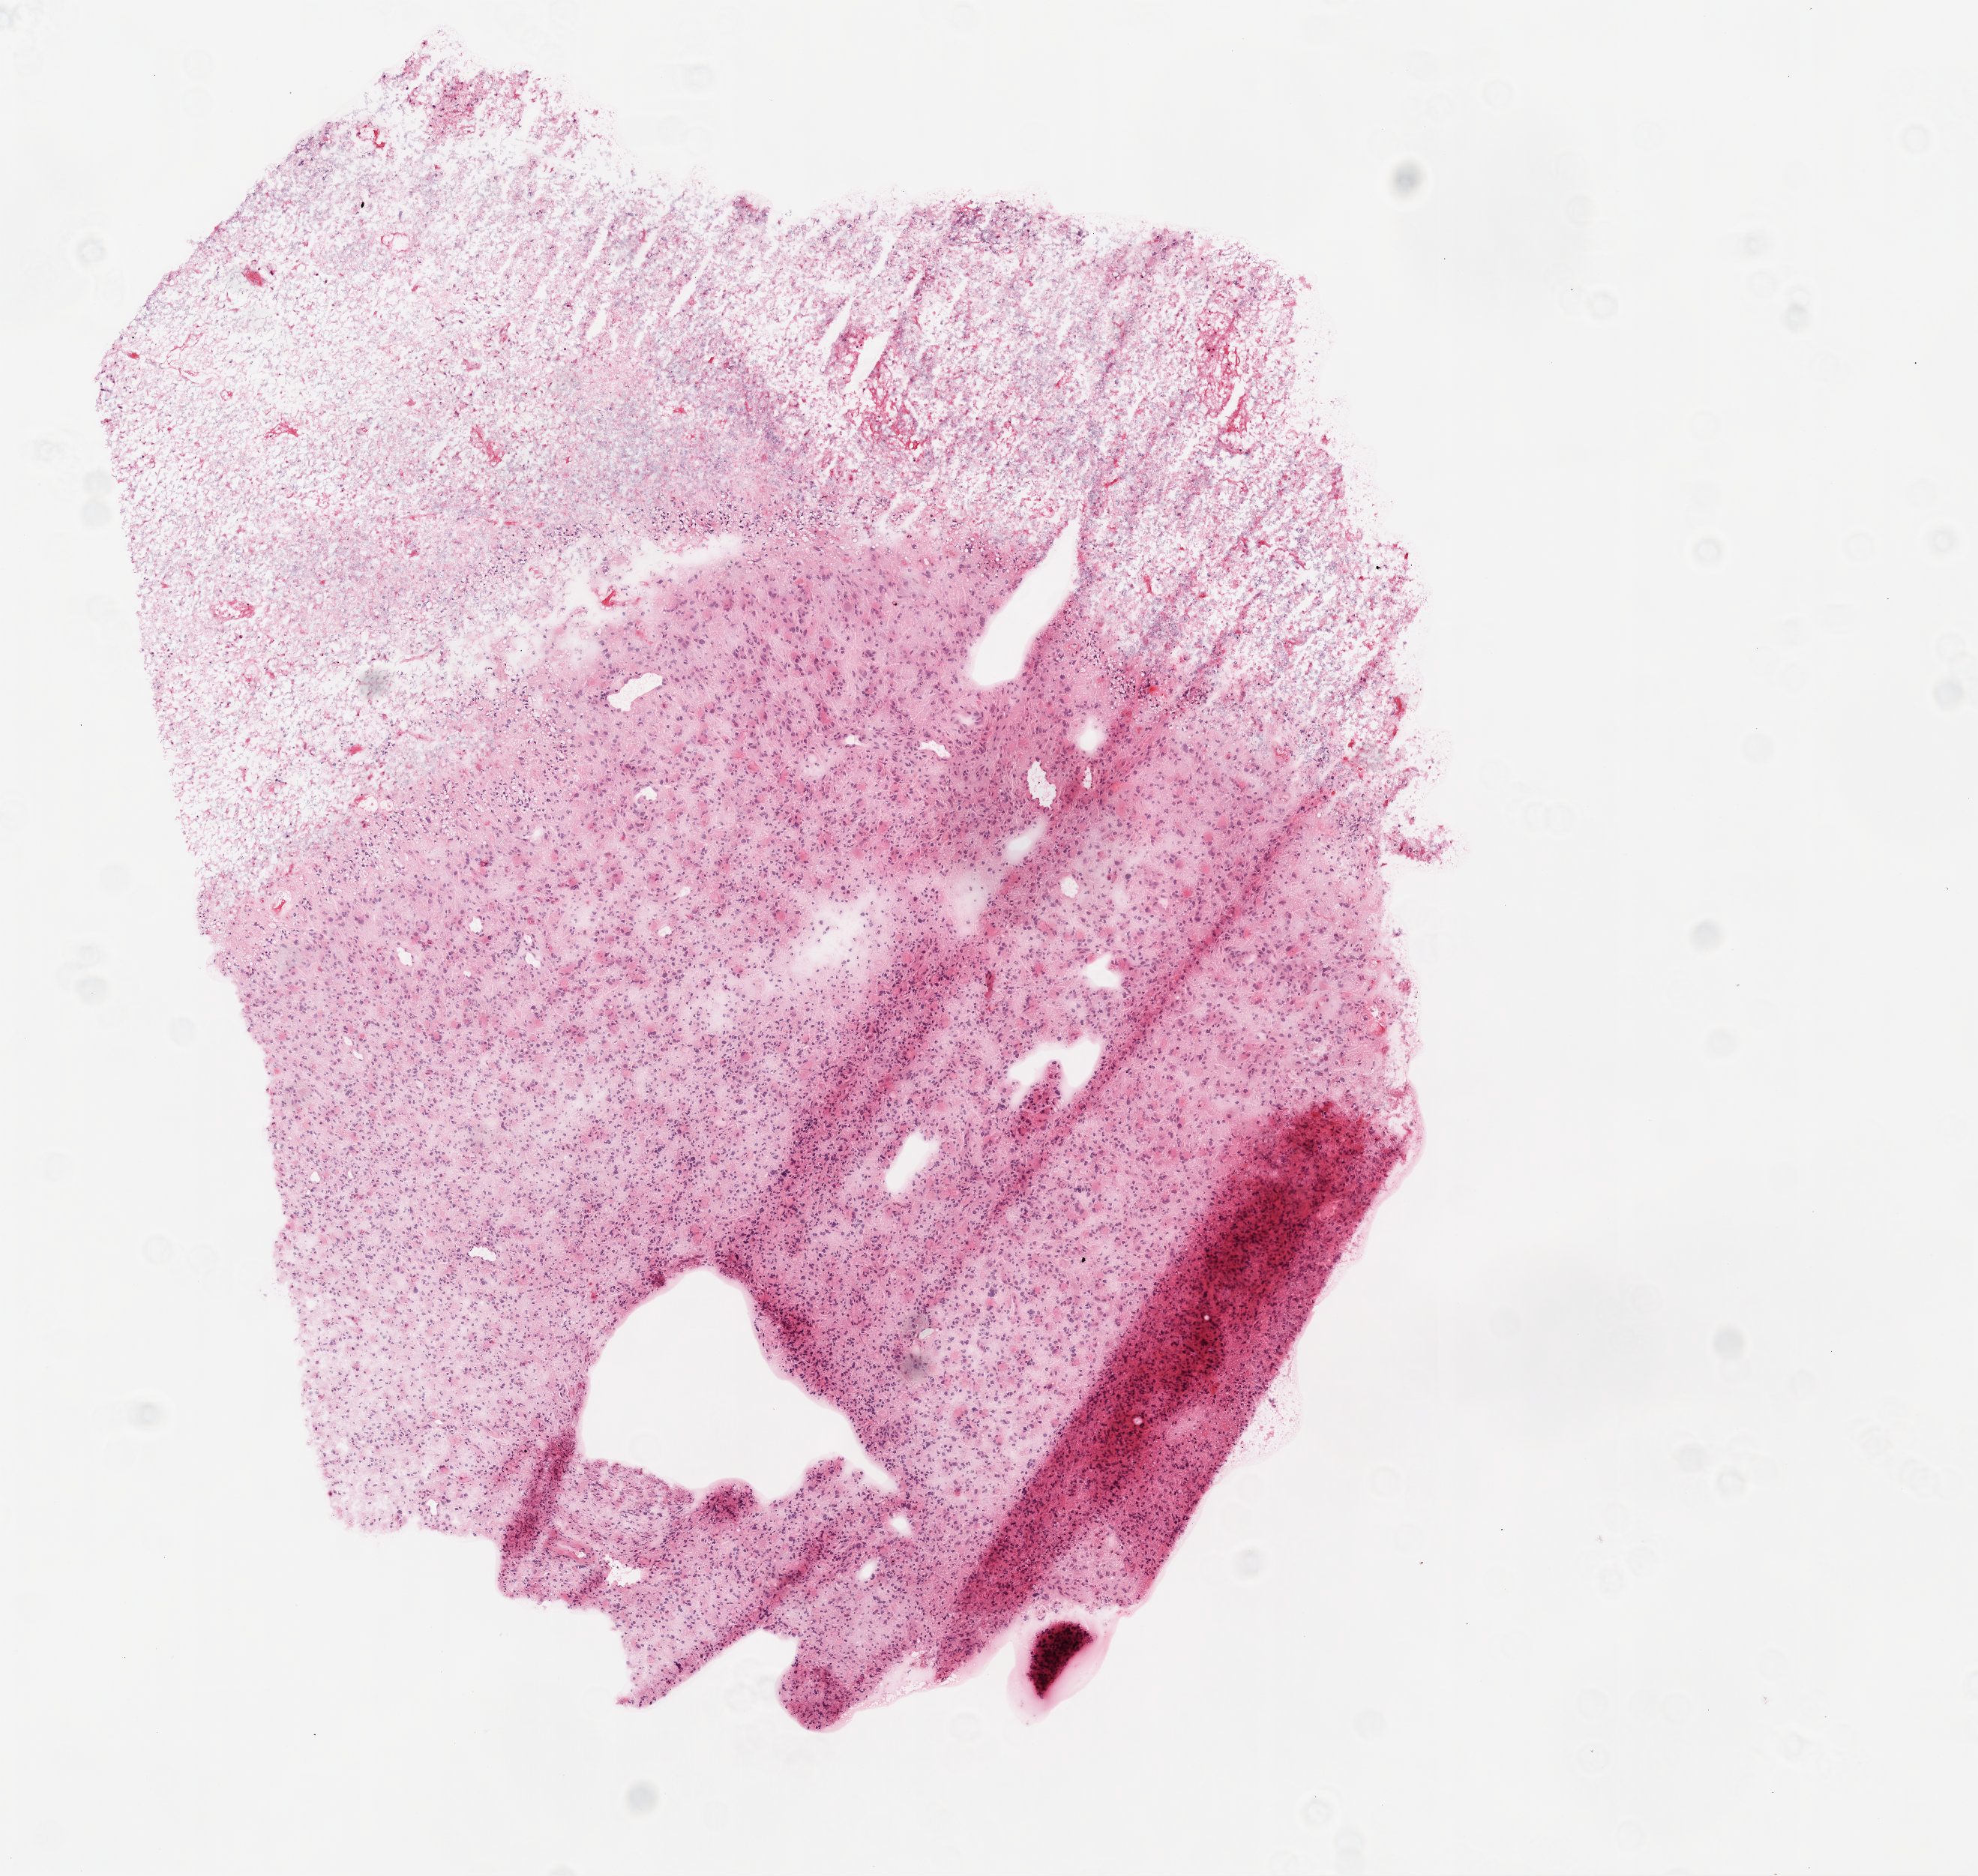
H&E whole-slide image, a low-resolution overview of the entire scanned area, about 5.3 x 5.0 mm (from a 20x scan); frozen section; primary tumour sample from the brain. Patient: male, age at initial diagnosis 76 years. Slide review estimates, as recorded: tumour cells 70%, tumour nuclei 80%.
Pathologic diagnosis: Glioblastoma.